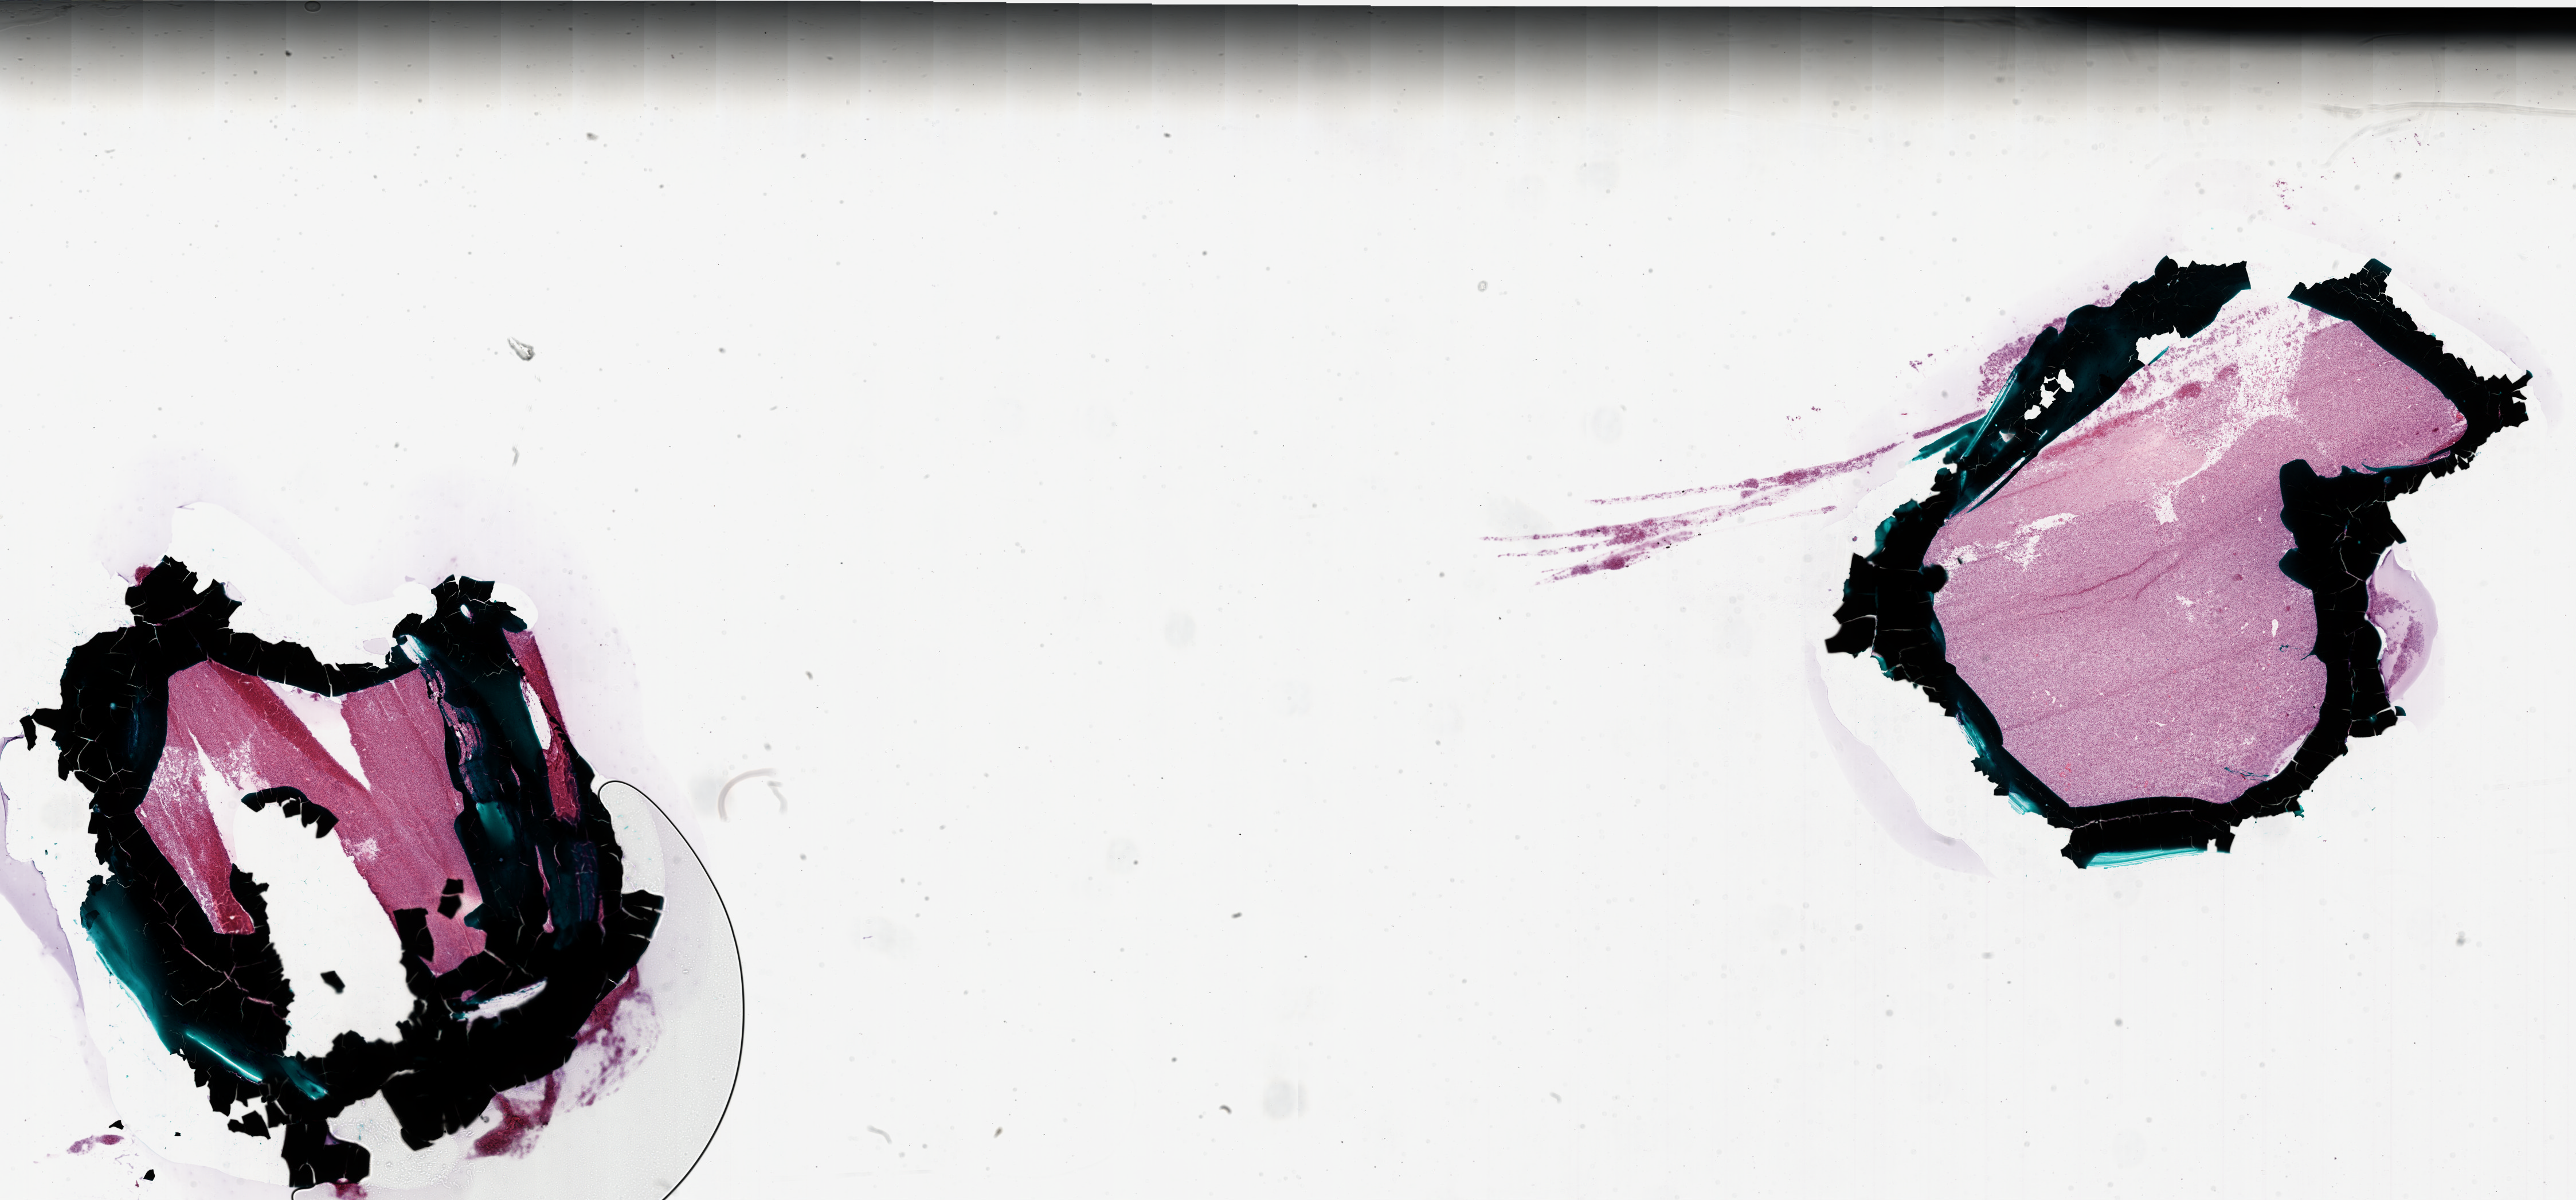
Digitized H&E tissue section (whole slide) — shown as a low-resolution overview of the whole scanned area (about 36.0 x 16.7 mm), frozen section, brain, primary tumour sample. Patient: female, age at initial diagnosis 63 years. Pathologist review of this section (percent, as recorded): tumour cells 85%, tumour nuclei 100%, normal cells 0%, stromal cells 0%, necrosis 15%. Infiltration values recorded for this section: lymphocyte infiltration 0%, monocyte infiltration 0%, neutrophil infiltration 0%.
Pathologic diagnosis: Glioblastoma.